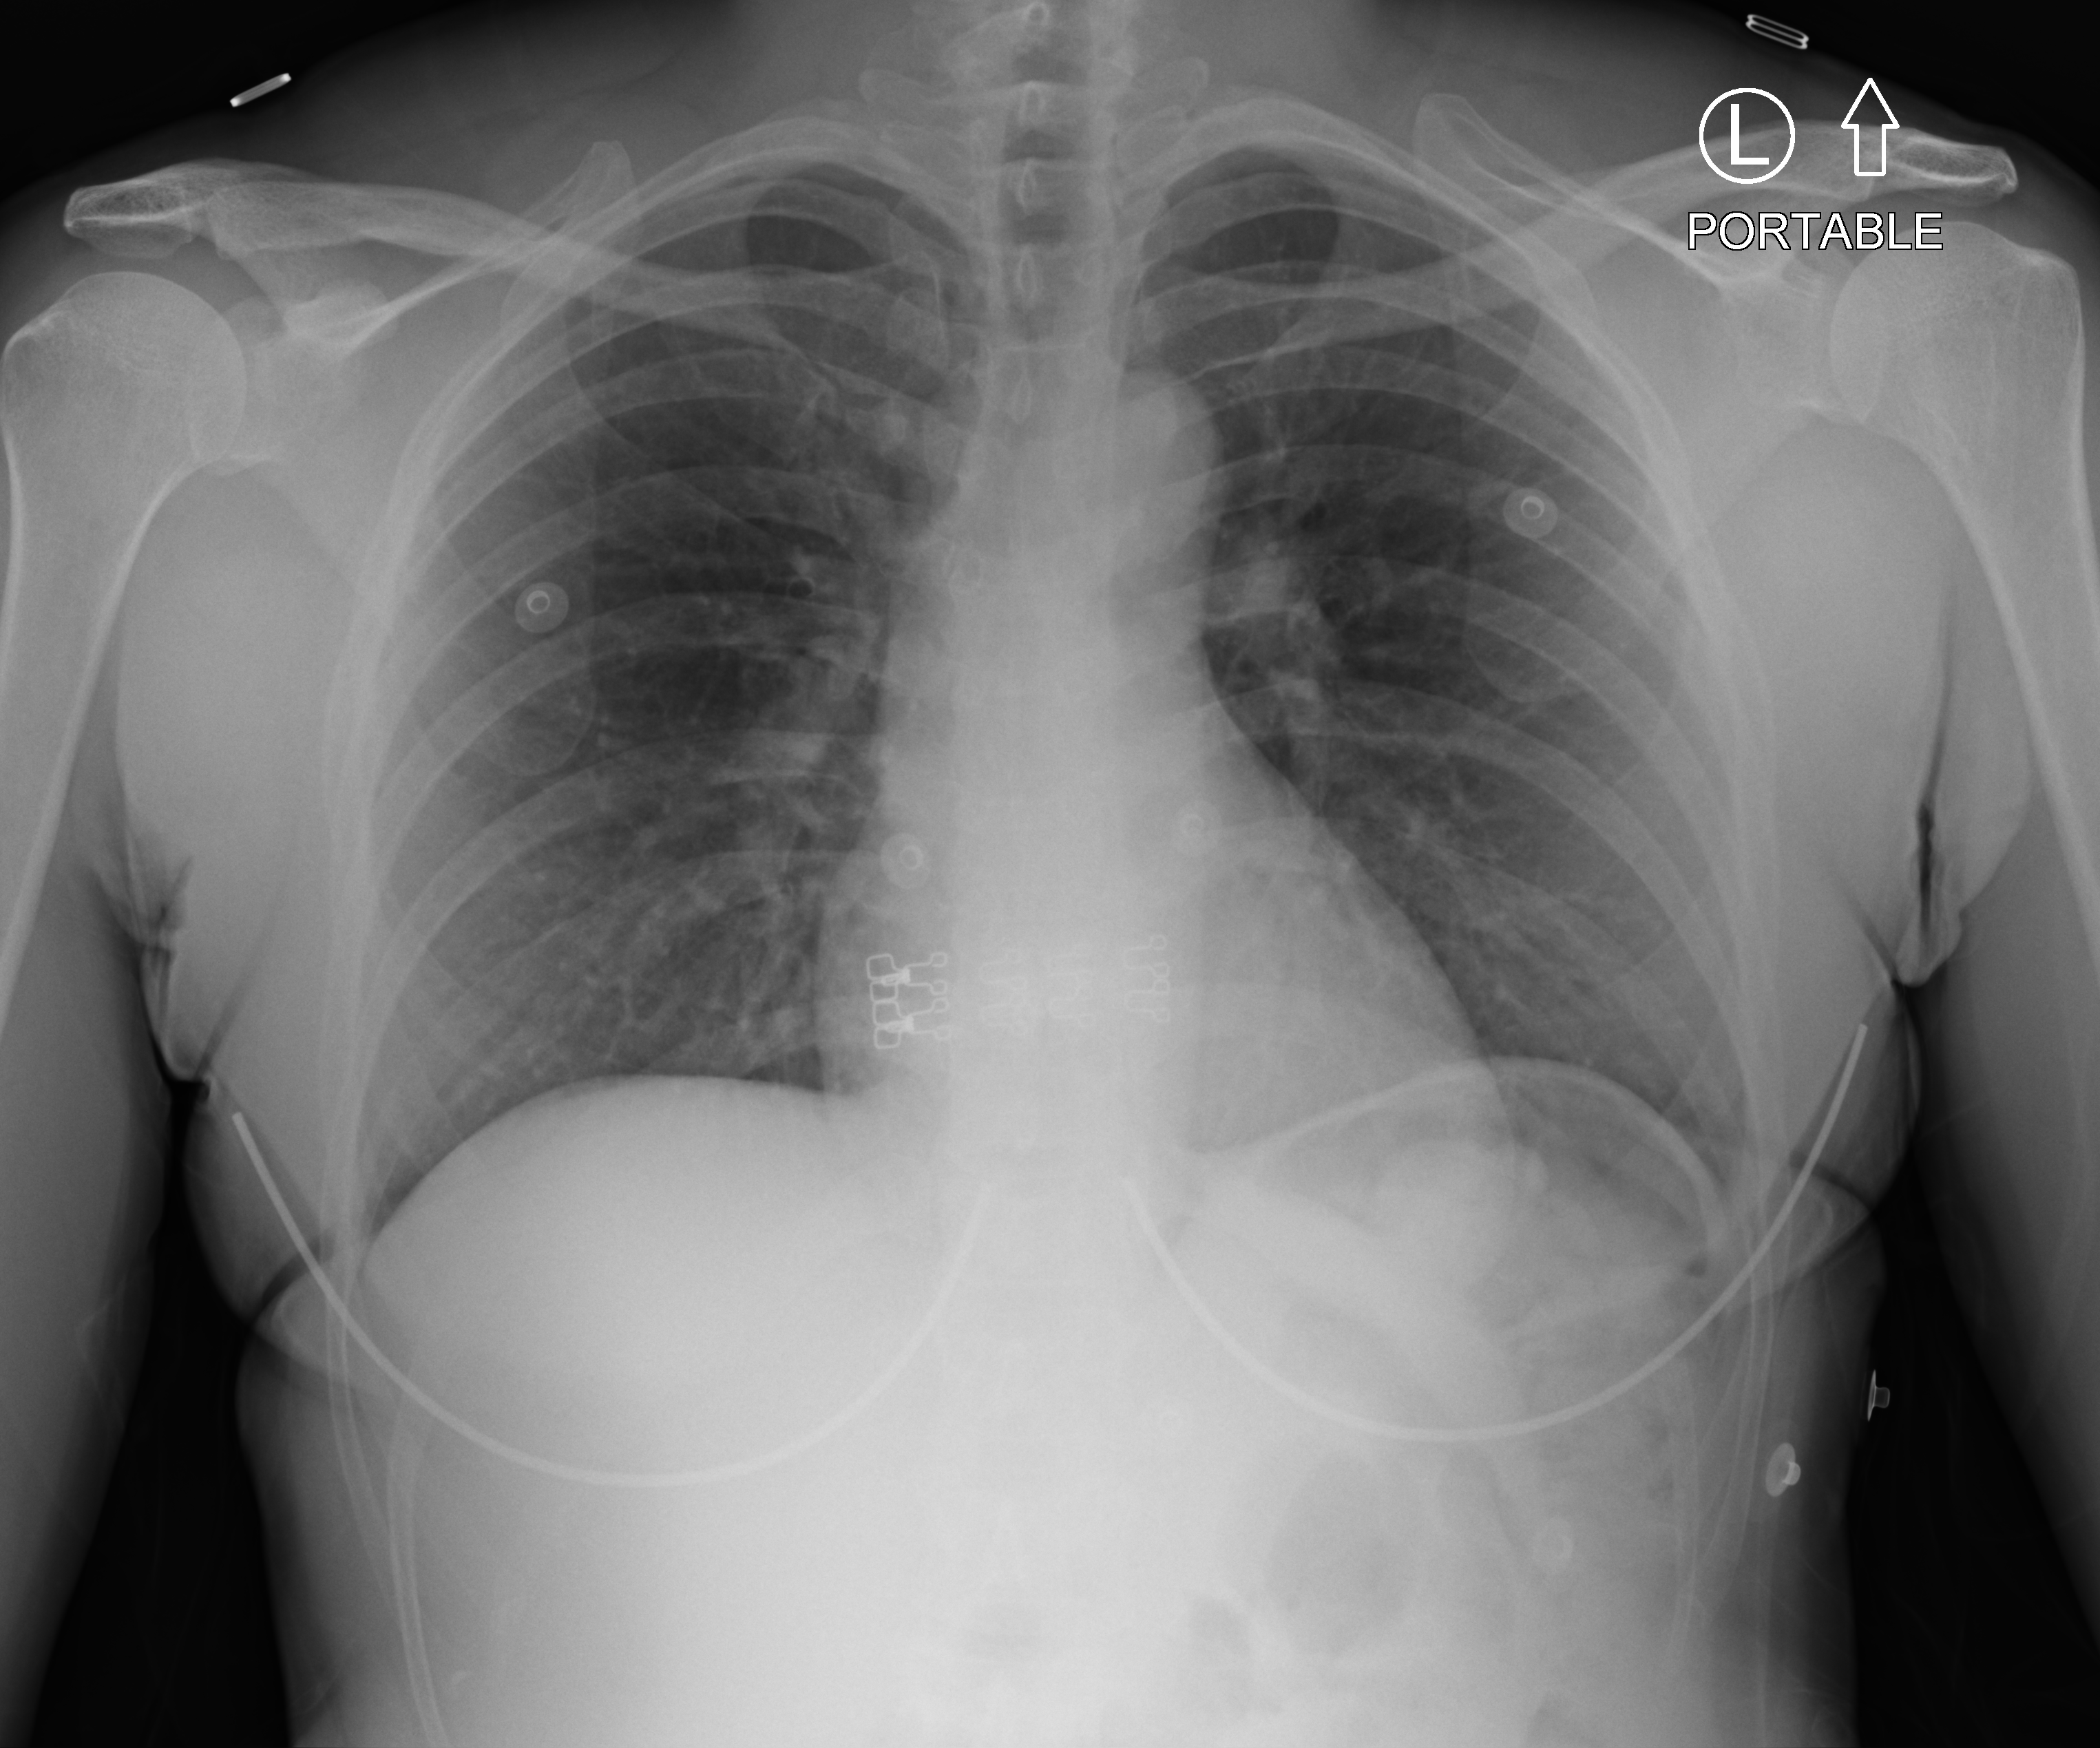
Chest X-ray (portable); anteroposterior (AP) projection. Female patient hospitalised with COVID-19, age 18–59 years.
Hospital-stay facts (about this admission, not read from this image; timing relative to this image not recorded): length of hospital stay: 1 day.